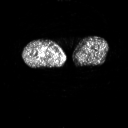
FDG PET of an extremity soft-tissue mass (from a PET/CT study), one axial slice. Position 232 of 311 along the scan axis. 128 × 128 image matrix, field of view 700 × 700 mm. Male patient, age 50 years. Case-level facts recorded for this patient, not image findings: histological type: undifferentiated - pleiomorphic; grade: high; site of the primary tumour: right thigh.
Annotated regions visible in this slice (expert contour drawn on MRI and transferred to this co-registered scan by the dataset authors):
- gross tumour volume including surrounding oedema: bounding box [x1, y1, x2, y2] px = [43, 52, 47, 57]